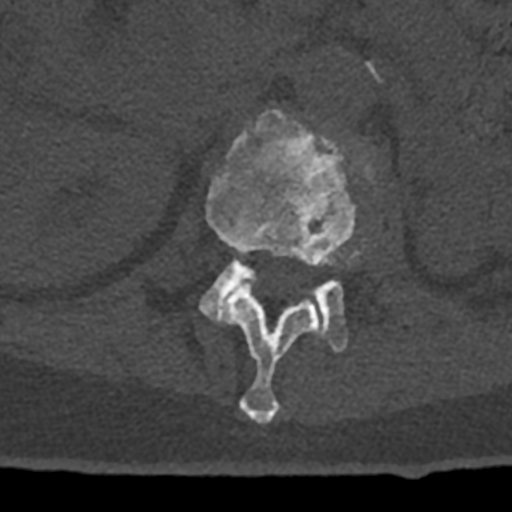
CT including the spine, one axial slice; reconstruction kernel Br40s/3; 120 kVp; bone window (W 1800 / L 400 HU); 0.5 mm slice thickness; 512 × 512 image matrix, field of view 160 × 160 mm. Patient: male, 74 years. From the clinical record (not read from this slice): primary cancer: renal; vertebrae with lytic lesions (as recorded): T10, L1, L2, L3, L4, L5.
Outlined on this slice (semi-automatically segmented with operator editing):
- L1 vertebra: bounding box (x1, y1, x2, y2) in pixels: (206, 110, 357, 424)
- L2 vertebra: (199, 243, 365, 353)